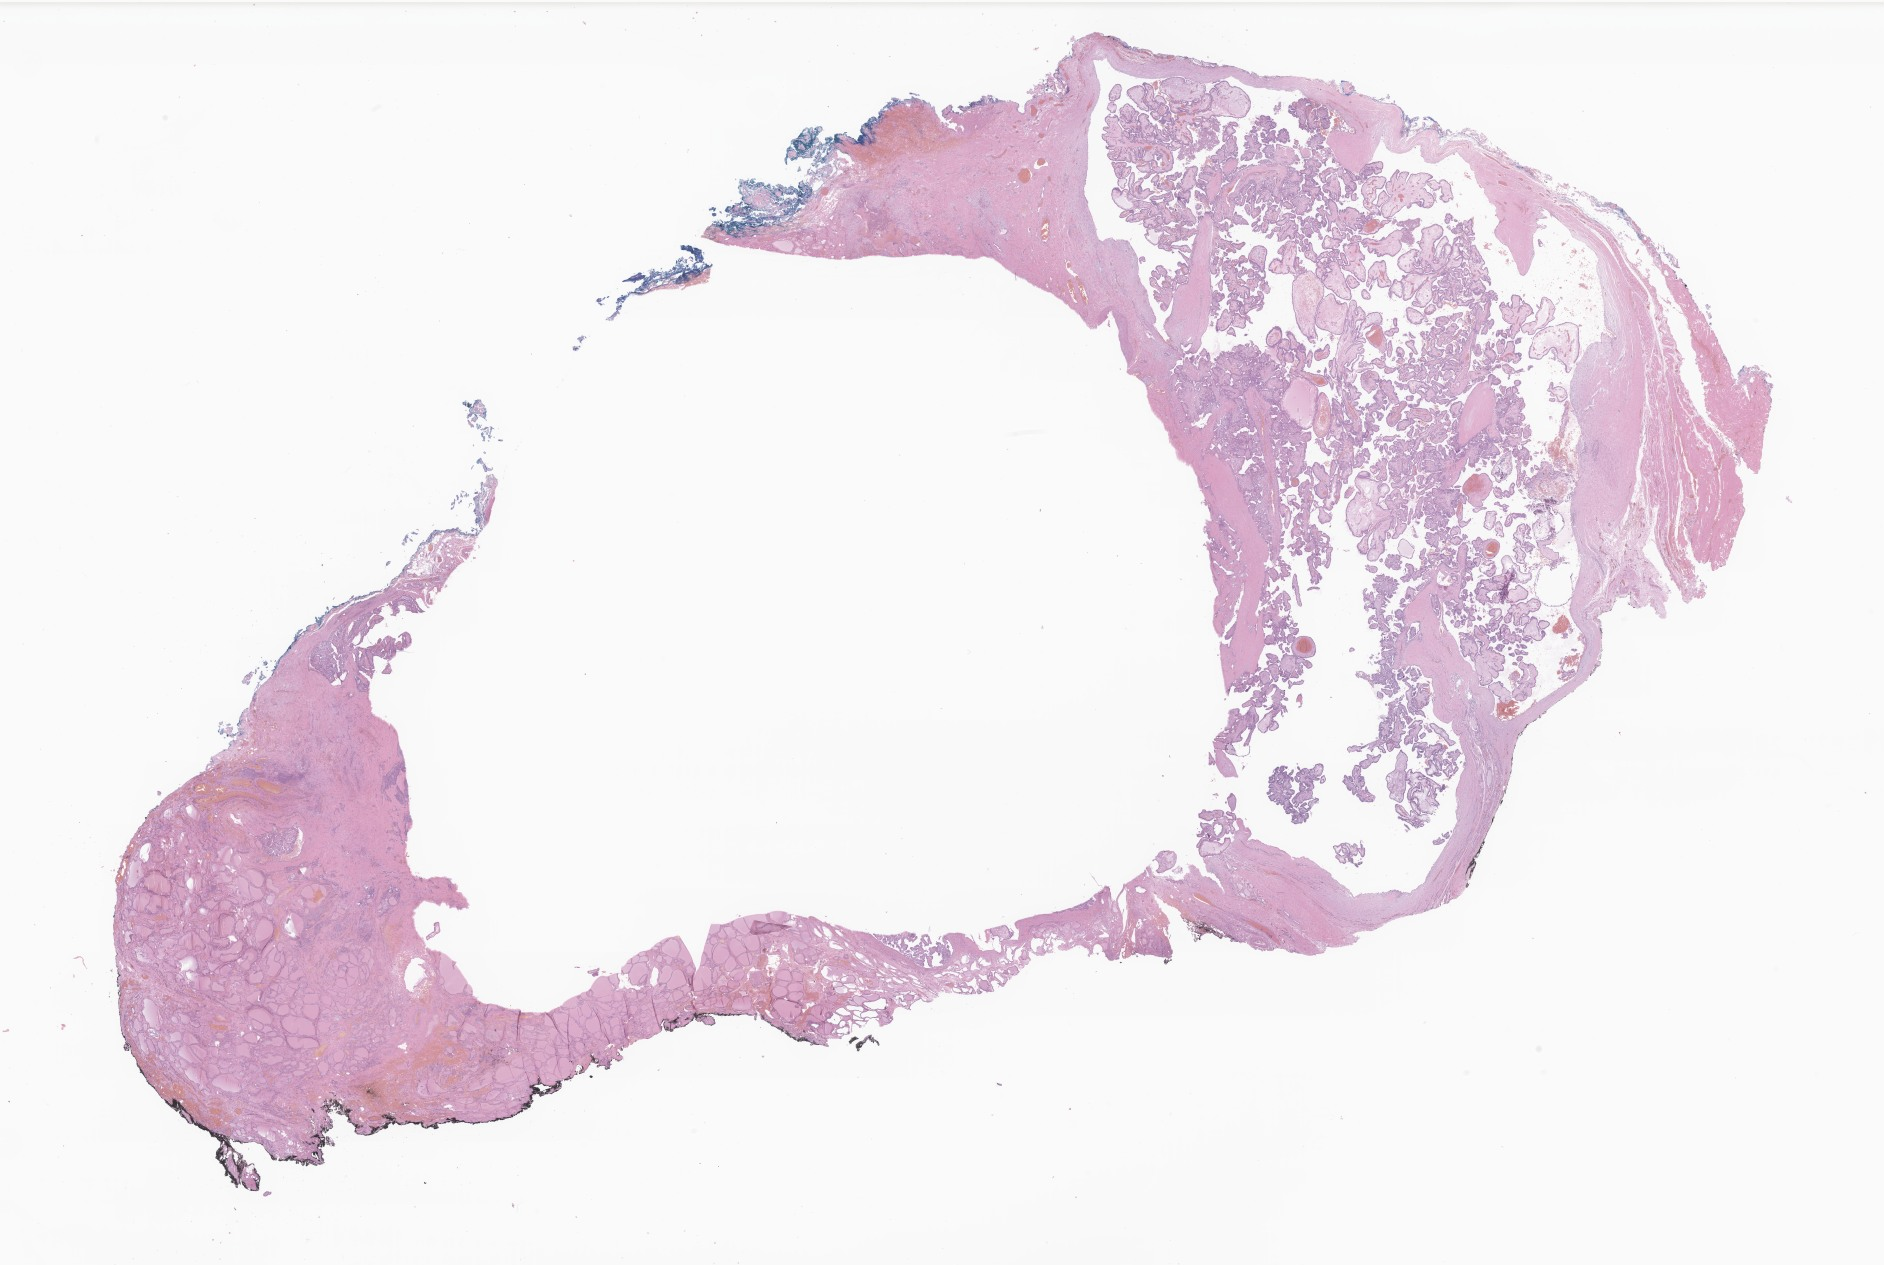
Haematoxylin and eosin whole-slide image of tumor tissue from the thyroid — shown as a low-resolution overview of the whole scanned area (about 31.8 x 21.3 mm); FFPE section. Female patient, age 179 months (14 years 11 months).
Recorded diagnosis: Papillary carcinoma, NOS.